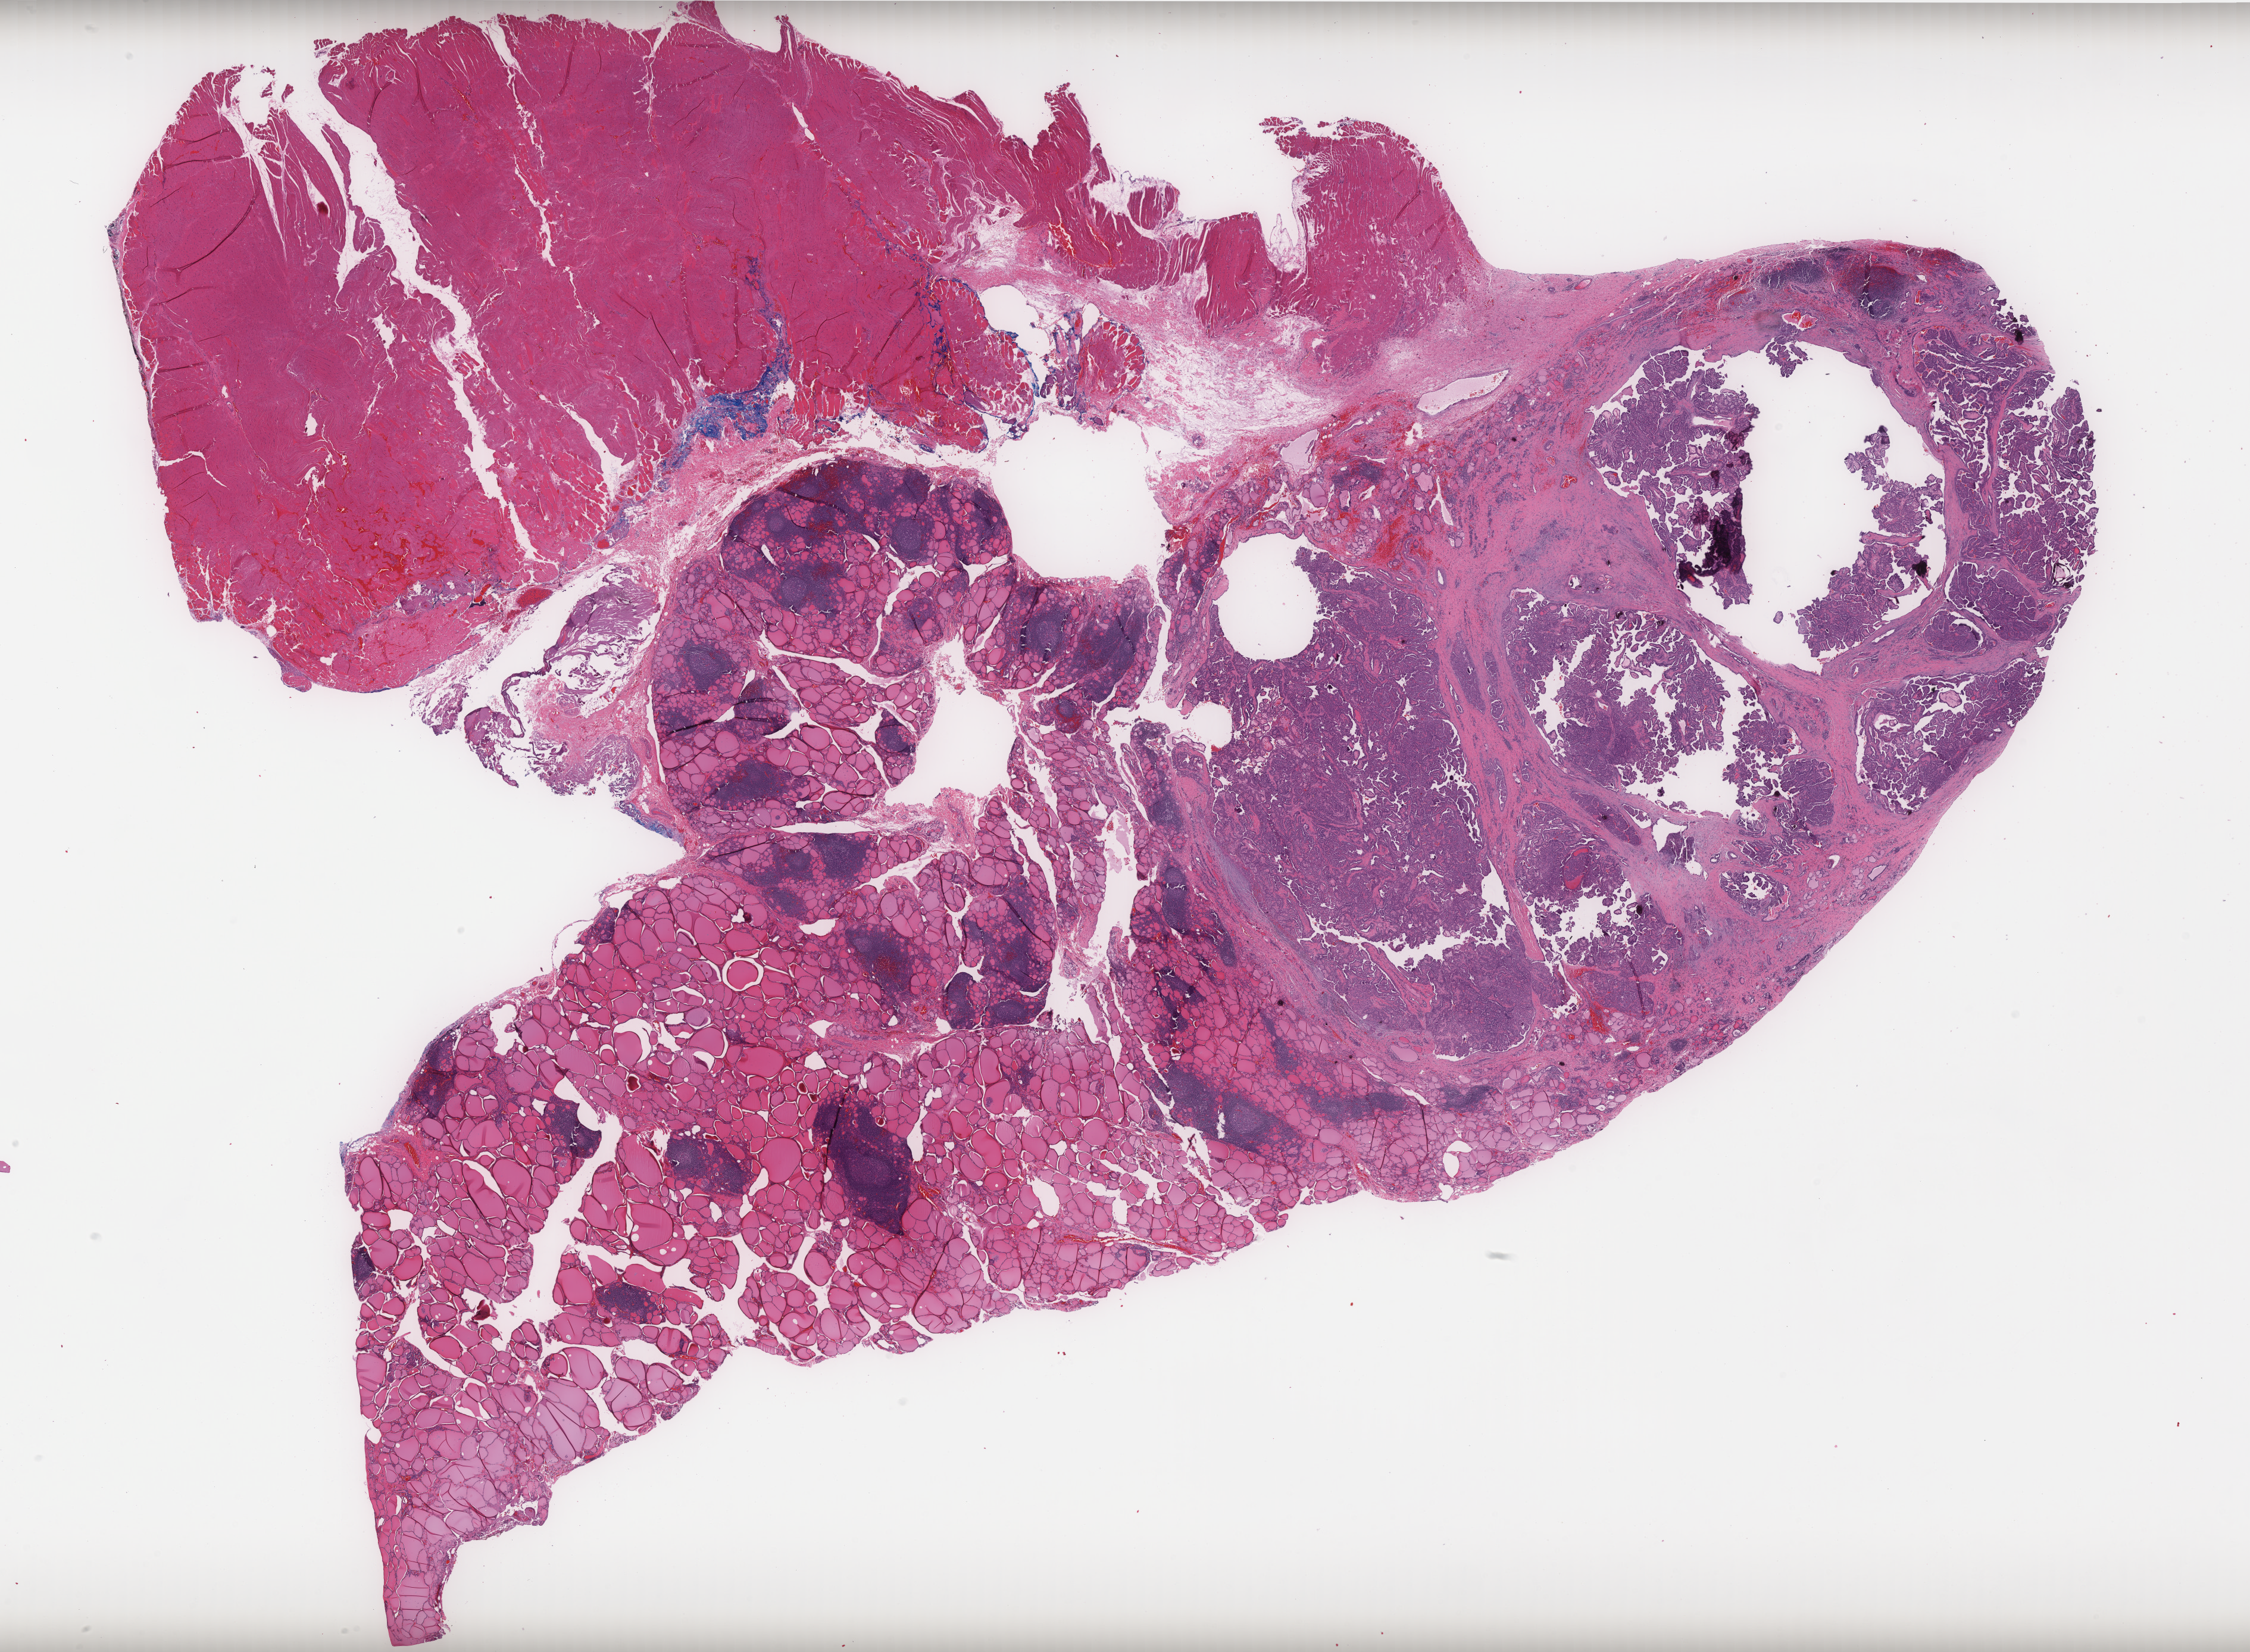
Hematoxylin and eosin (H&E) stained whole-slide image, a low-resolution overview of the entire scanned area, about 30.3 x 22.2 mm (from a 40x scan). Formalin-fixed paraffin-embedded (FFPE) diagnostic section. Sample: primary tumour, thyroid. Female, age 20 years at initial diagnosis.
AJCC pathologic stage: I (7th edition). Histologic diagnosis: Papillary adenocarcinoma, NOS (thyroid gland).